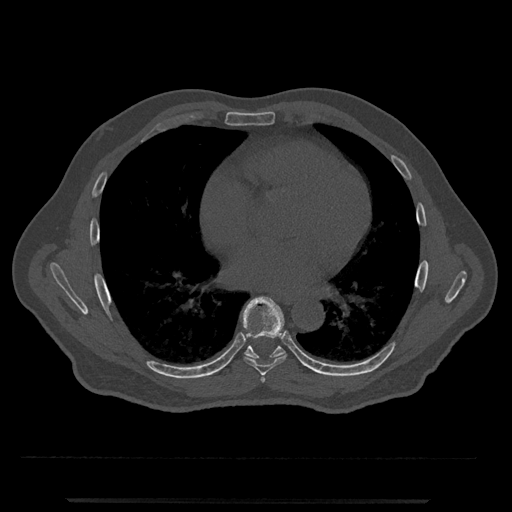
CT including the spine, one axial slice; position 661 of 797 along the scan axis; reconstruction kernel Br40s/3; 120 kVp; bone window (W 1800 / L 400 HU); 0.5 mm slice thickness; 512 × 512 image matrix, field of view 419 × 419 mm. Male patient, age 63 years. Case-level facts recorded for this patient, not image findings: primary cancer: prostate.
Outlined on this slice (semi-automatically segmented with operator editing):
- T6 vertebra: box from (x=261, y=375) to (x=265, y=383) px
- T7 vertebra: (x=242, y=296)–(x=287, y=375)
- T8 vertebra: (x=244, y=333)–(x=285, y=359)